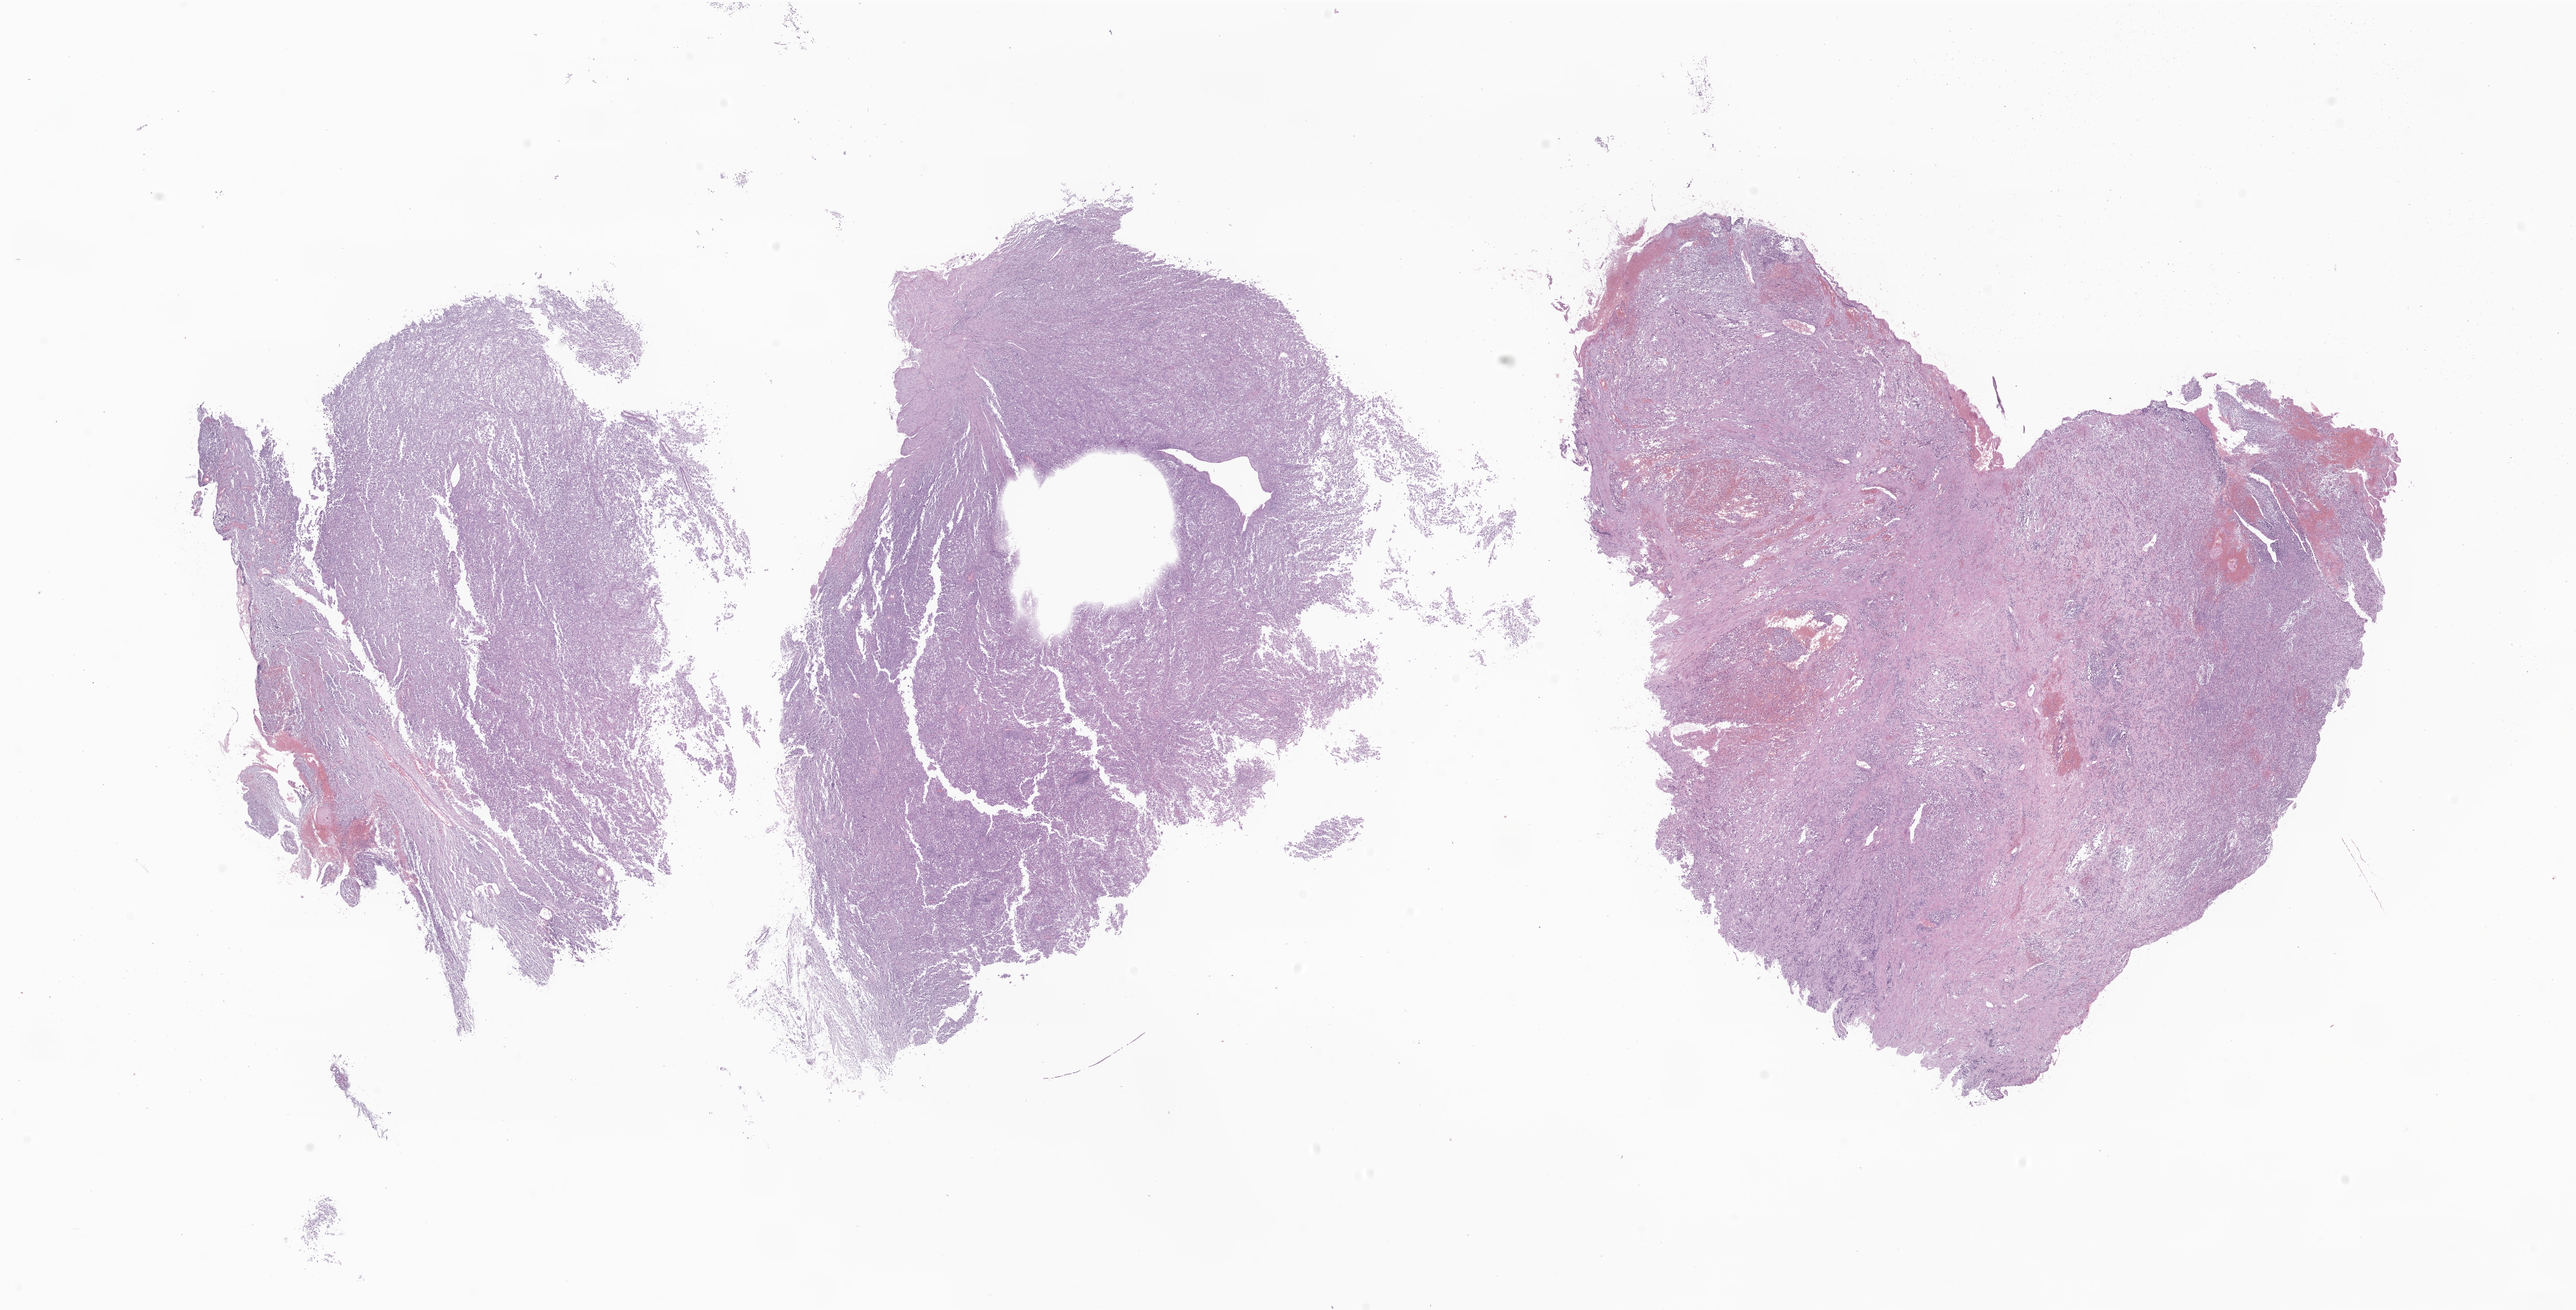
Whole-slide image, H&E stain of tumor tissue from the uterine adnexa — shown as a low-resolution overview of the whole scanned area (about 28.6 x 14.5 mm), formalin-fixed, paraffin-embedded (FFPE) tissue. Female patient, age 152 months (12 years 8 months).
• diagnosis (ICD-O-3 morphology term): Alveolar rhabdomyosarcoma